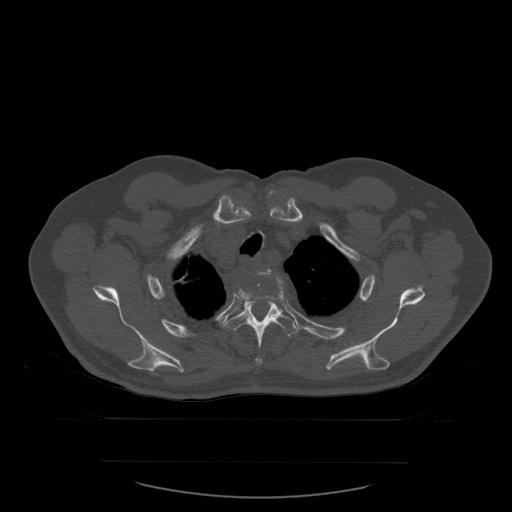
CT including the spine, one axial slice. Slice 450 of 590 in the series (ordered by position). Bone window (W 1800 / L 400 HU). 1.25 mm slice thickness. 512 × 512 image matrix, field of view 479 × 479 mm. Patient age 71 years. Case-level facts recorded for this patient, not image findings: primary cancer: lung; vertebrae with lytic lesions (as recorded): T1, T2, L5, S1.
Structures marked on this image (semi-automatically segmented with operator editing):
- T2 vertebra: bounding box (x1, y1, x2, y2) in pixels: (267, 270, 279, 280)
- T3 vertebra: (238, 272, 284, 300)
- T4 vertebra: (223, 292, 299, 366)